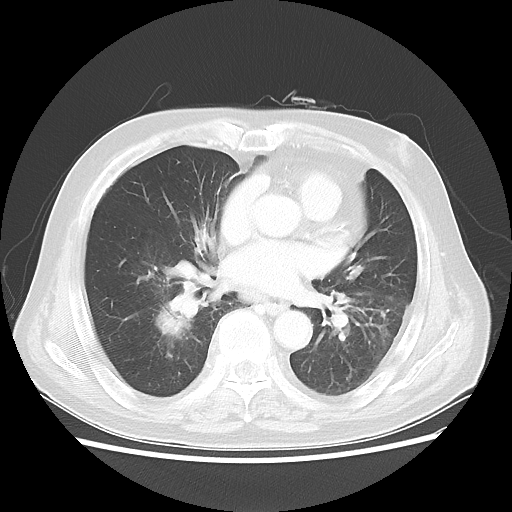
Chest CT, one axial slice. Reconstruction kernel LUNG. 100 kVp. Lung window (W 1500 / L -600 HU). 512 × 512 image matrix, field of view 359 × 359 mm. Patient: male, 83 years. From the clinical record (not read from this slice): clinical TNM (as recorded): T2 N3 M0.
Annotated regions visible in this slice (bounding box drawn by a radiologist):
- lung tumour (recorded histology: adenocarcinoma): box from (x=151, y=292) to (x=195, y=346) px